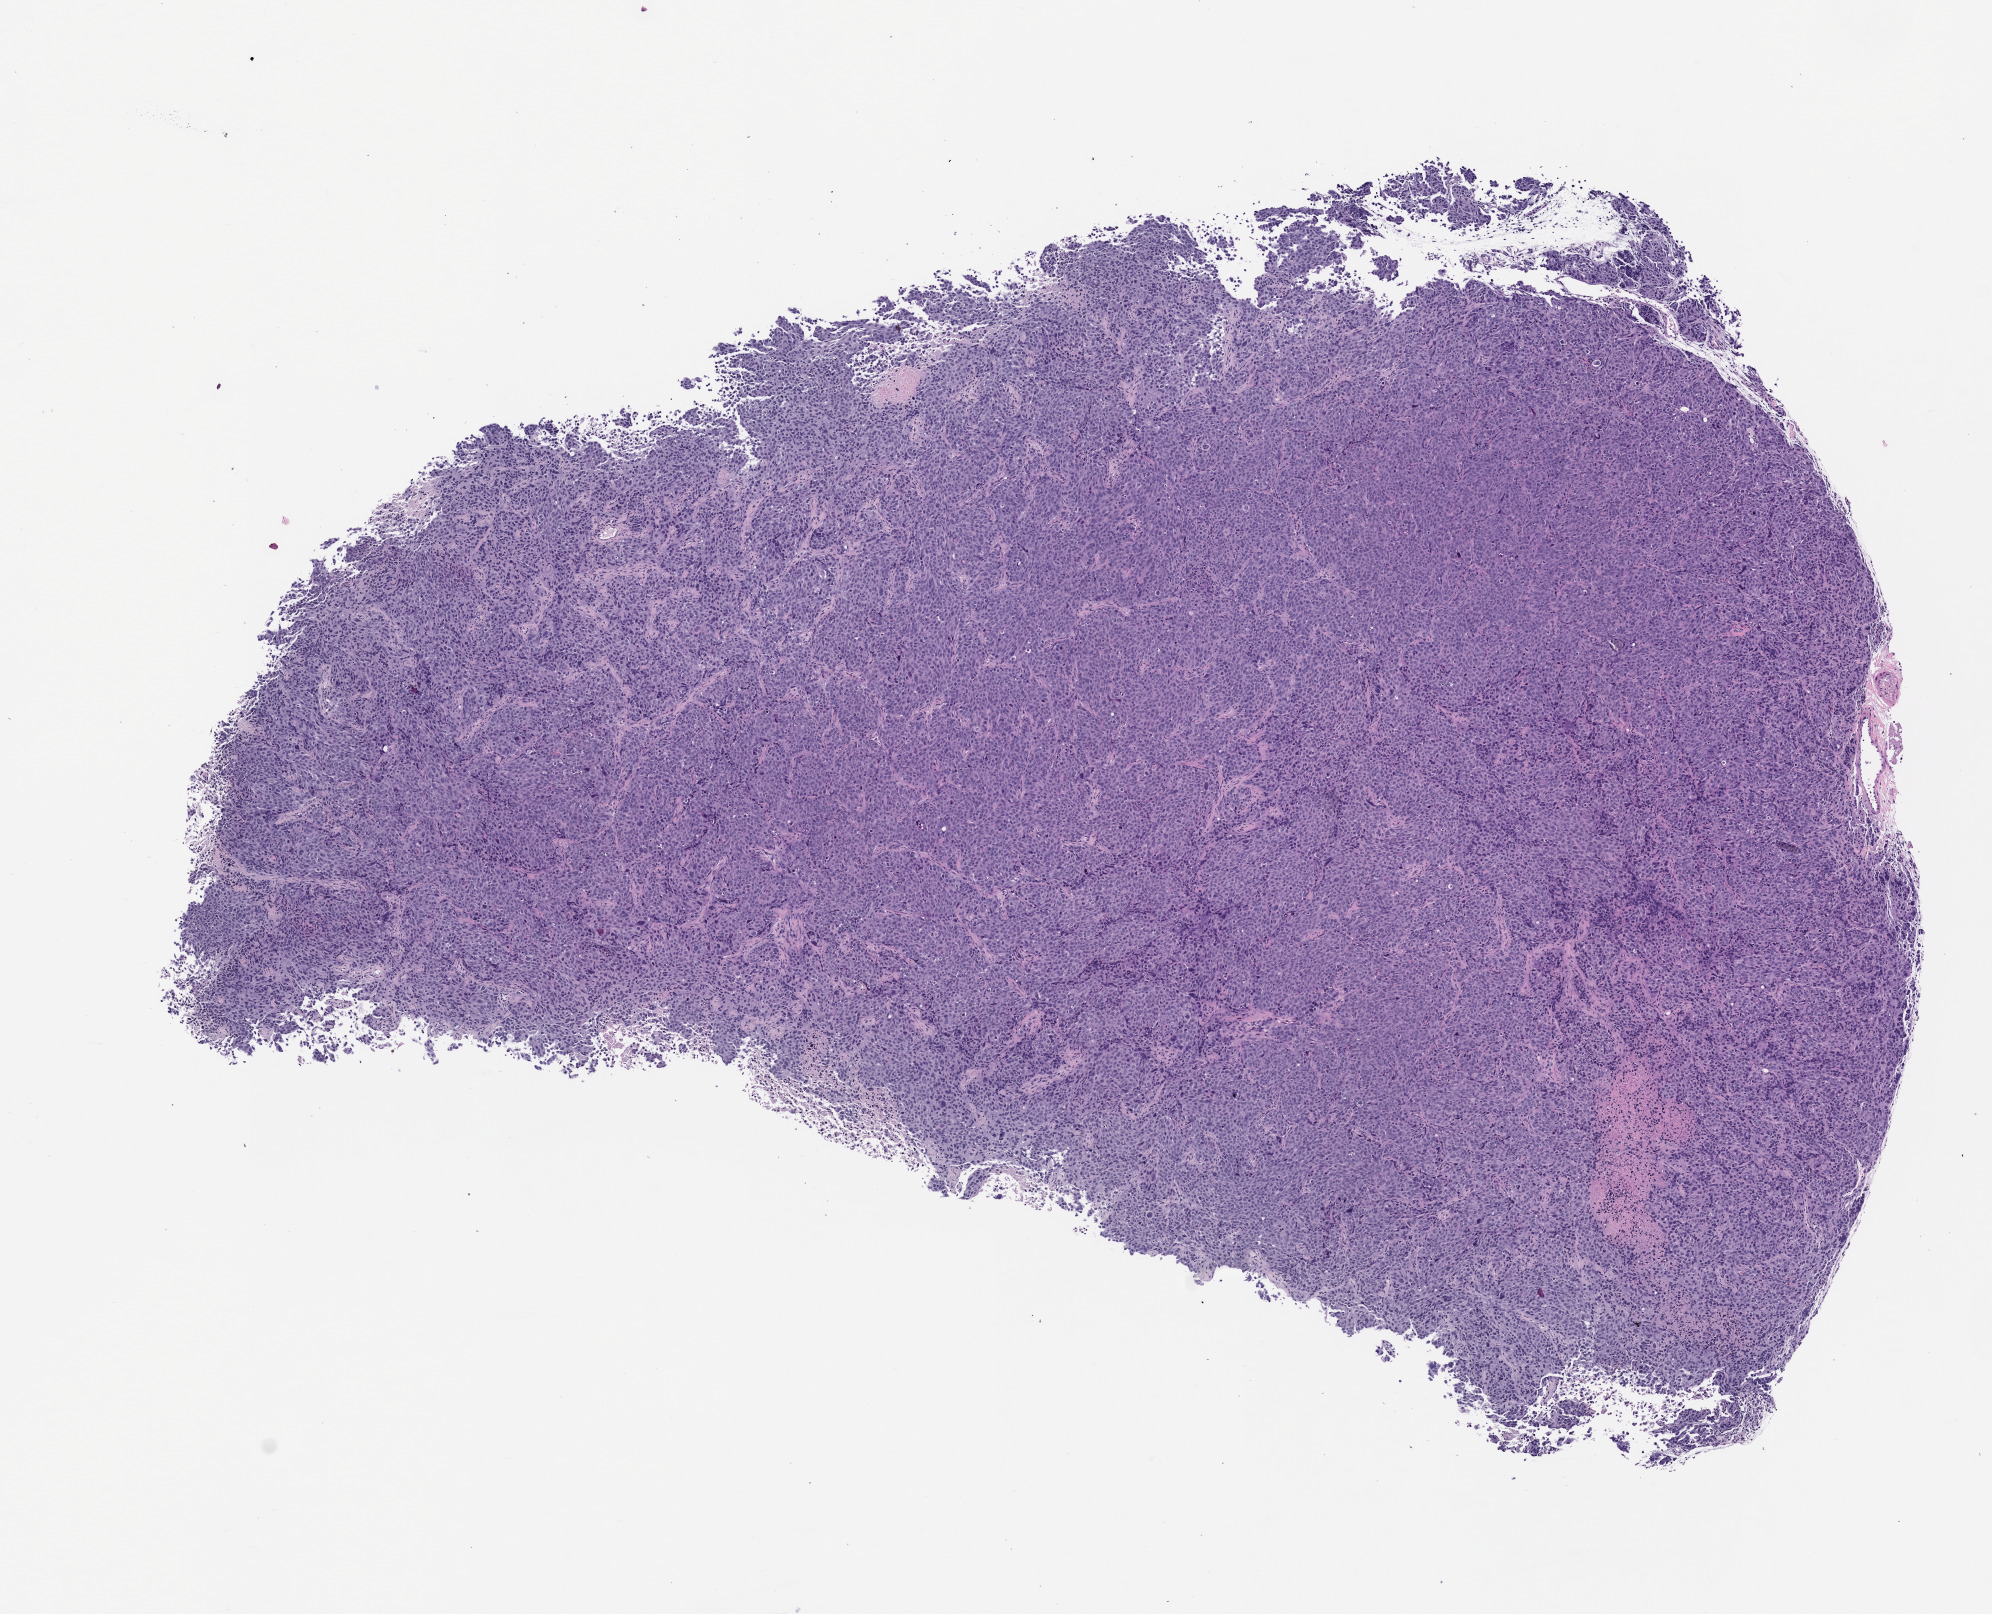
Hematoxylin and eosin (H&E) whole-slide image of a patient-derived xenograft (PDX) tumor grown in a mouse, passage 1, whole scanned area (about 8.0 x 6.5 mm) shown as a low-resolution overview, formalin-fixed paraffin-embedded section, tumor site category: lung.
Originating patient diagnosis: Lung Squamous Cell Carcinoma.